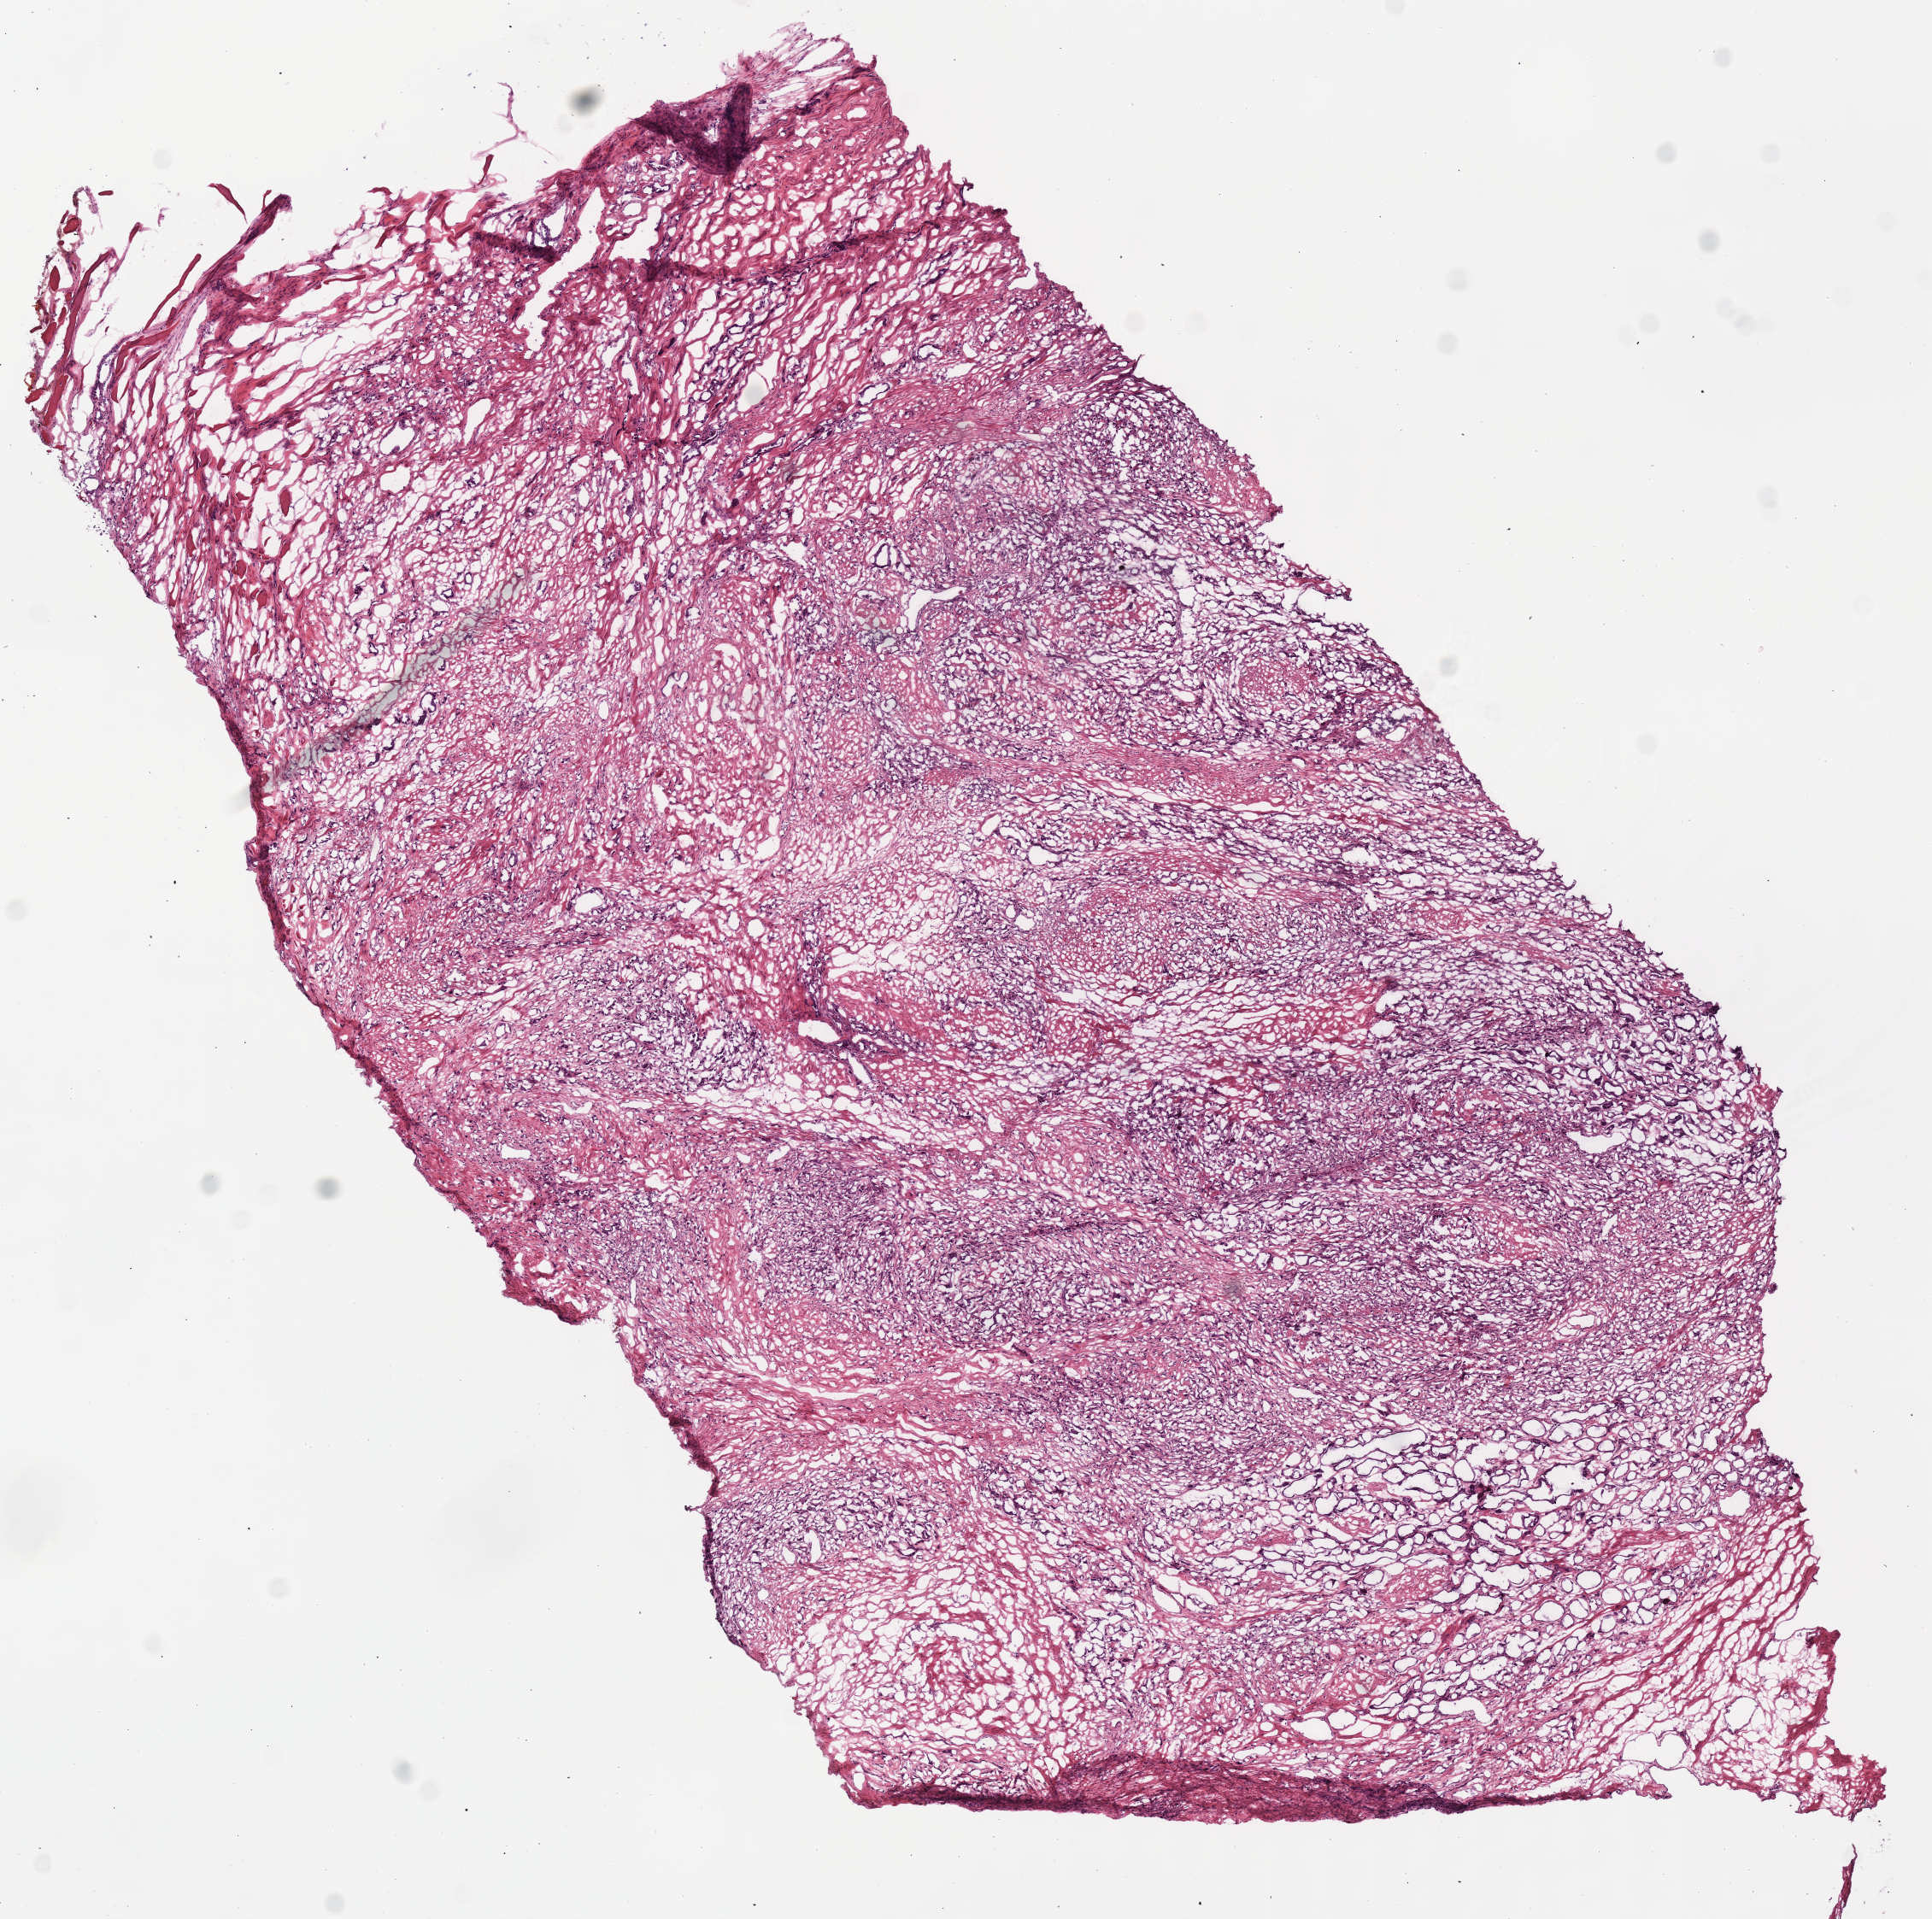
Digitized H&E tissue section (whole slide) — shown as a low-resolution overview of the whole scanned area (about 8.9 x 8.8 mm, acquisition: 40x scan); frozen section from the top of the tissue portion; sample: primary tumour, prostate. Male patient; age at initial diagnosis 44 years.
Diagnosis: Acinar cell carcinoma (prostate gland).